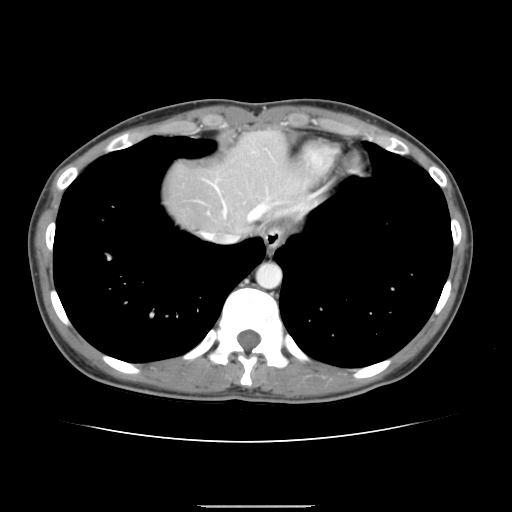
Contrast-enhanced abdominal CT, one axial slice. Position 131 of 150 along the scan axis. 120 kVp. Intravenous contrast given. Soft-tissue window (W 400 / L 40 HU). 512 × 512 image matrix. Female patient, age 32 years. Case-level facts recorded for this patient, not image findings: diagnosis: colorectal cancer liver metastases, imaged before liver resection; multiple liver metastases: yes; largest metastasis: 0.7 cm; disease in both lobes: no.
Outlined on this slice (manually delineated by an expert):
- hepatic veins: bounding box <202,181,269,243> (left, top, right, bottom; pixels)
- liver: <165,130,313,233>
- planned liver remnant (the part of the liver to remain after resection): <165,131,313,234>